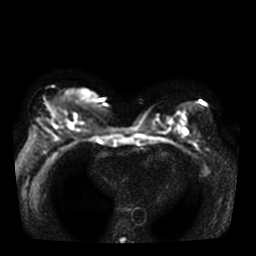
Breast MRI, one axial slice; slice 15 of 36 in the series (ordered by position); diffusion-weighted series; image 2 of 4 stored at this slice position (different b-values; order by instance number); 3 T; 256 × 256 image matrix, field of view 330 × 330 mm. Female patient.
Annotated regions visible in this slice (outlined manually by an expert reader):
- tumour on diffusion-weighted imaging: bounding box [x1, y1, x2, y2] px = [68, 123, 74, 129]